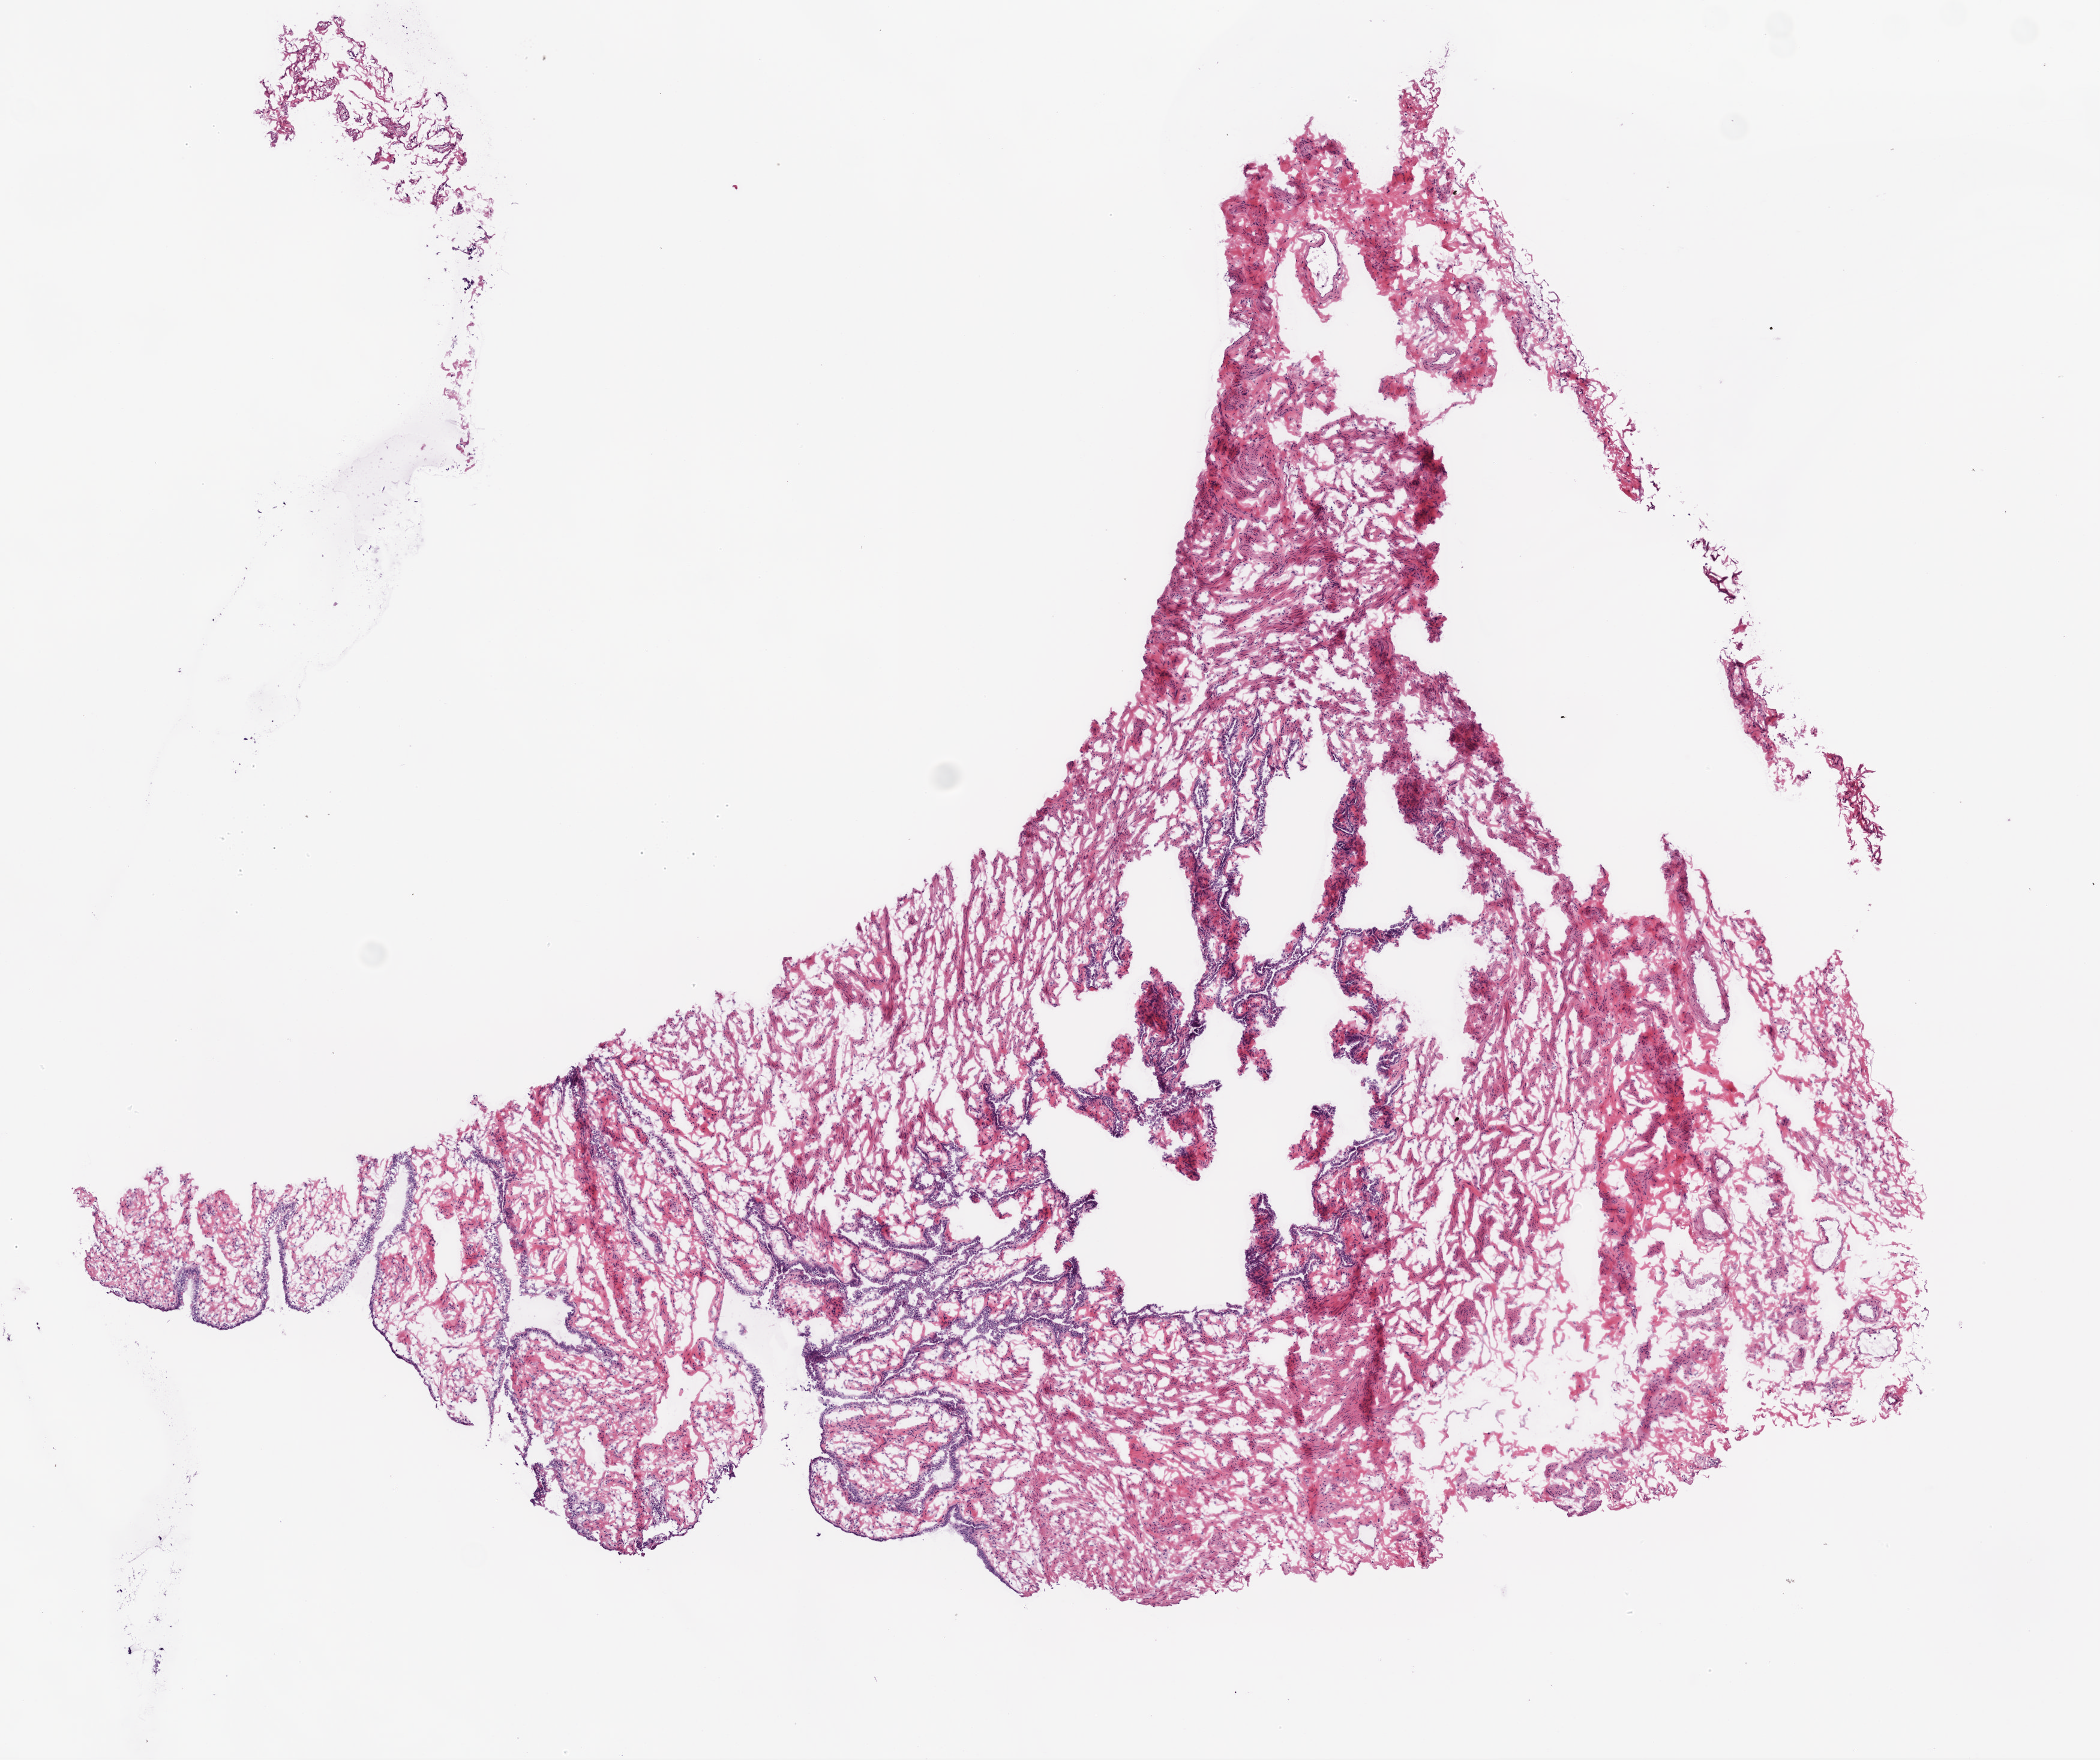
H&E whole-slide image, whole scanned area (about 7.0 x 5.9 mm) shown as a low-resolution overview. Frozen section from the bottom of the tissue portion. Ovary, solid tissue normal (non-tumour tissue) sample. Female, age 60 years at initial diagnosis.
This section: solid tissue normal (non-tumour) sample from the same patient. Patient diagnosis: Serous cystadenocarcinoma, NOS.